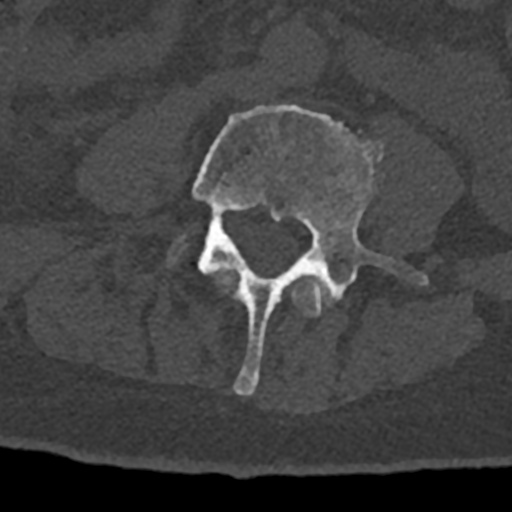
CT including the spine, one axial slice; slice 263 of 797 in the series (ordered by position); bone window (W 1800 / L 400 HU); 0.5 mm slice thickness; 512 × 512 image matrix. Patient: male, 74 years. Case-level facts recorded for this patient, not image findings: primary cancer: renal; vertebrae with lytic lesions (as recorded): T10, L1, L2, L3, L4, L5.
Annotated regions visible in this slice (semi-automatically segmented with operator editing):
- L3 vertebra: box from (x=212, y=270) to (x=332, y=317) px
- L4 vertebra: (x=189, y=105)–(x=428, y=395)
- L5 vertebra: (x=170, y=237)–(x=184, y=264)